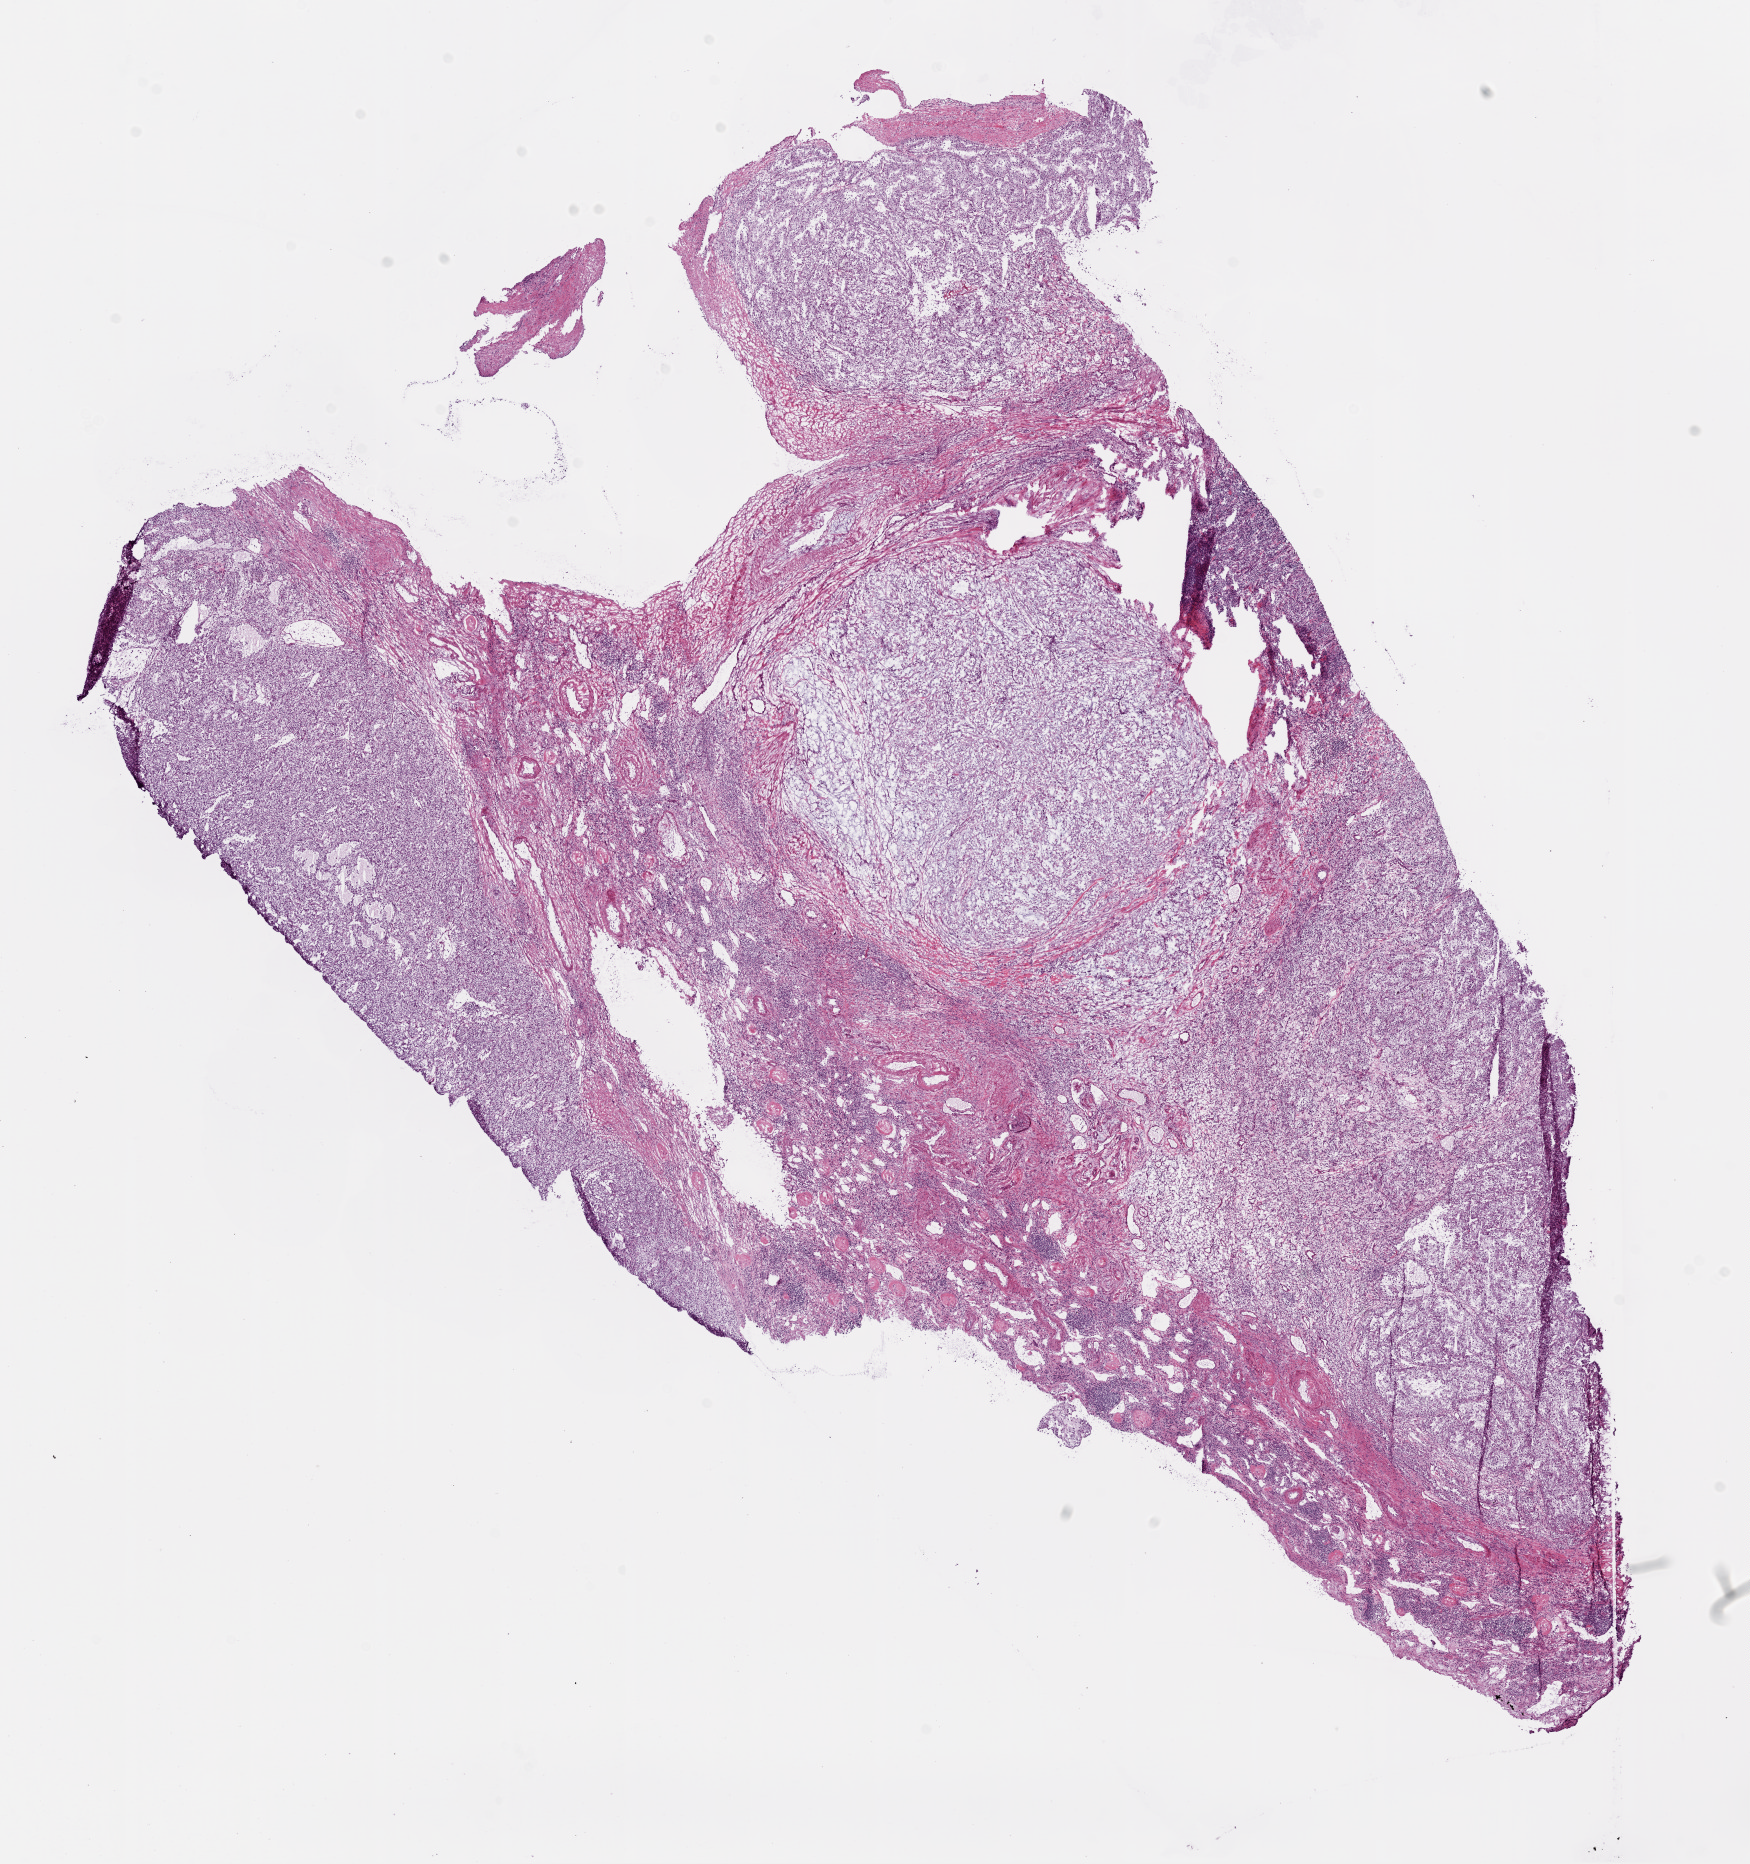
Whole-slide histology image, Hematoxylin and eosin (H&E) stained — a low-resolution overview of the entire scanned area, about 14.0 x 15.0 mm, frozen section from the top of the tissue portion, primary tumour sample from the kidney. Female patient; age at initial diagnosis 62 years. Histologic grade: G3 (poorly differentiated). Composition of this section per pathologist review: tumour cells 80%, tumour nuclei 72%, normal cells 0%, stromal cells 20%, necrosis 0%.
Diagnosis: Clear cell adenocarcinoma, NOS. Laterality: right. AJCC pathologic stage: III (6th edition). TNM: T3a NX M0.